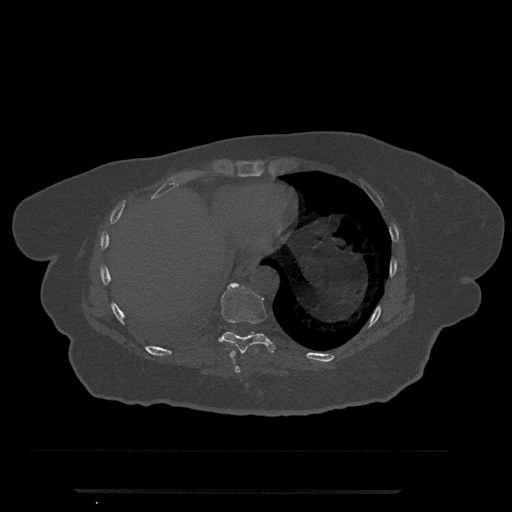
CT including the spine, one axial slice. Position 333 of 797 along the scan axis. Reconstruction kernel Br40s/3. 120 kVp. Bone window (W 1800 / L 400 HU). 512 × 512 image matrix, field of view 440 × 440 mm. Female patient, age 51 years. Case-level facts recorded for this patient, not image findings: primary cancer: neuro; vertebrae with lytic lesions (as recorded): T8.
Structures marked on this image (semi-automatic segmentation, software-assisted and operator-edited):
- T8 vertebra: bounding box [x1, y1, x2, y2] px = [234, 364, 241, 373]
- T9 vertebra: [209, 283, 276, 358]